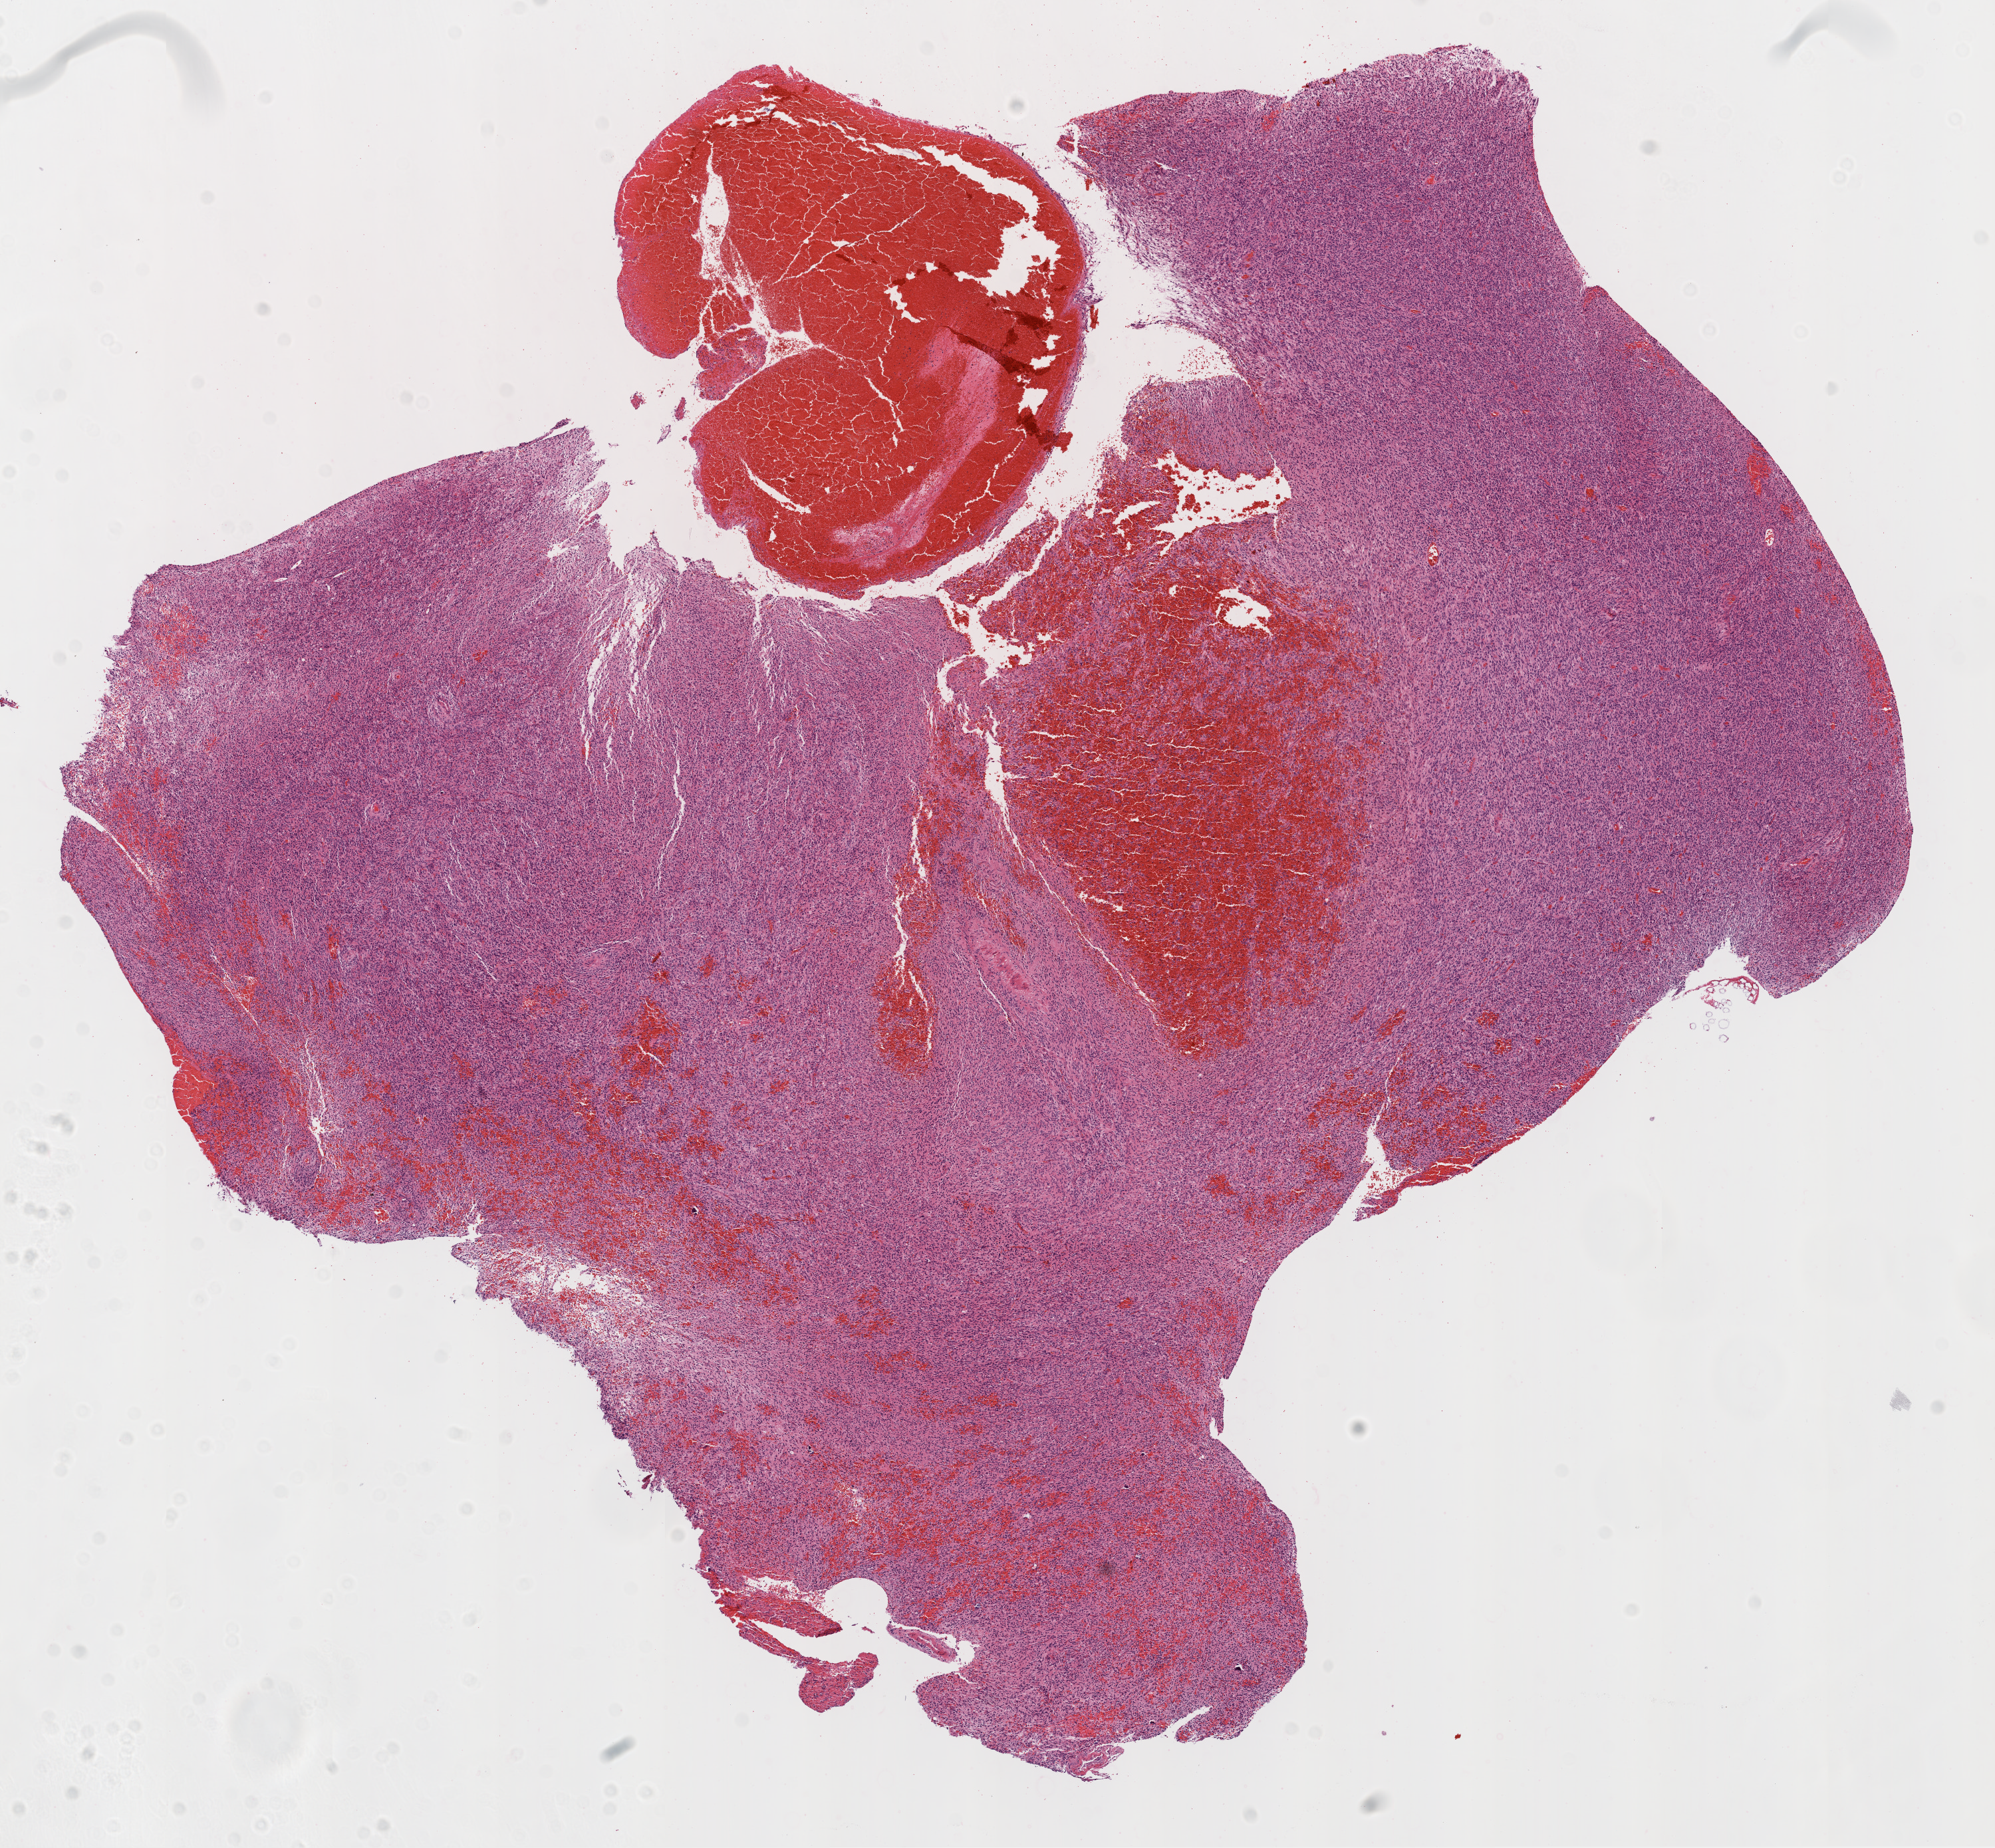
Digitized Hematoxylin and eosin (H&E) stained tissue section (whole slide) — shown as a low-resolution overview of the whole scanned area (about 12.0 x 11.1 mm), FFPE section, sample: primary tumour, brain. Female patient; age at initial diagnosis 53 years.
Diagnosis: Glioblastoma.